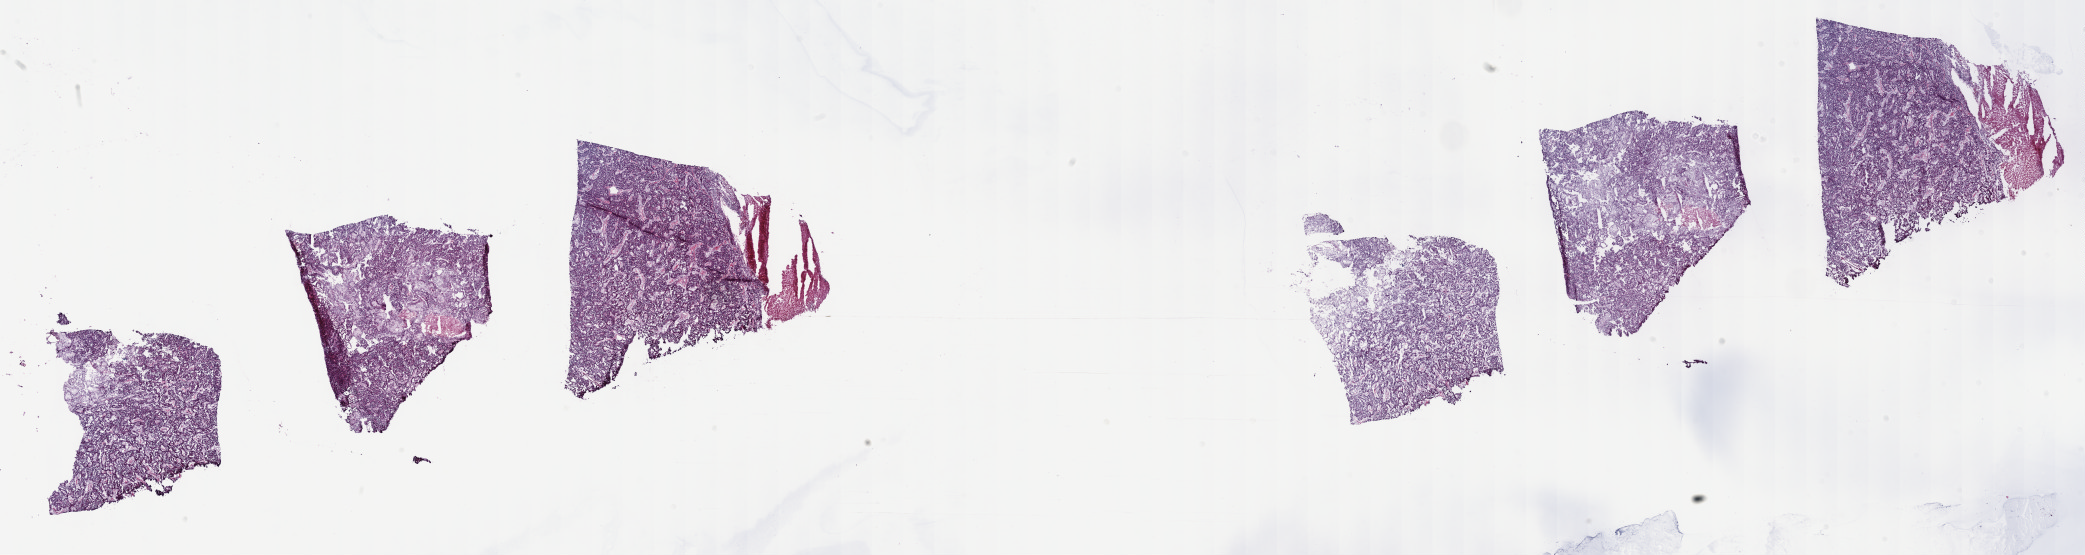
Digitized H&E-stained tissue section (whole slide) — shown as a low-resolution overview of the whole scanned area (about 33.7 x 9.0 mm). Frozen section from the top of the tissue portion. Kidney, primary tumour sample. Male patient; age at initial diagnosis 64 years. Pathologist review of this section (percent, as recorded): tumour cells 65%, tumour nuclei 70%, normal cells 0%, stromal cells 30%, necrosis 5%. Inflammatory infiltration, as recorded: lymphocyte infiltration 0%, monocyte infiltration 10%, neutrophil infiltration 0%.
- TNM: T1a NX MX
- laterality: left
- AJCC pathologic stage: I (7th edition)
- histologic diagnosis: Papillary adenocarcinoma, NOS